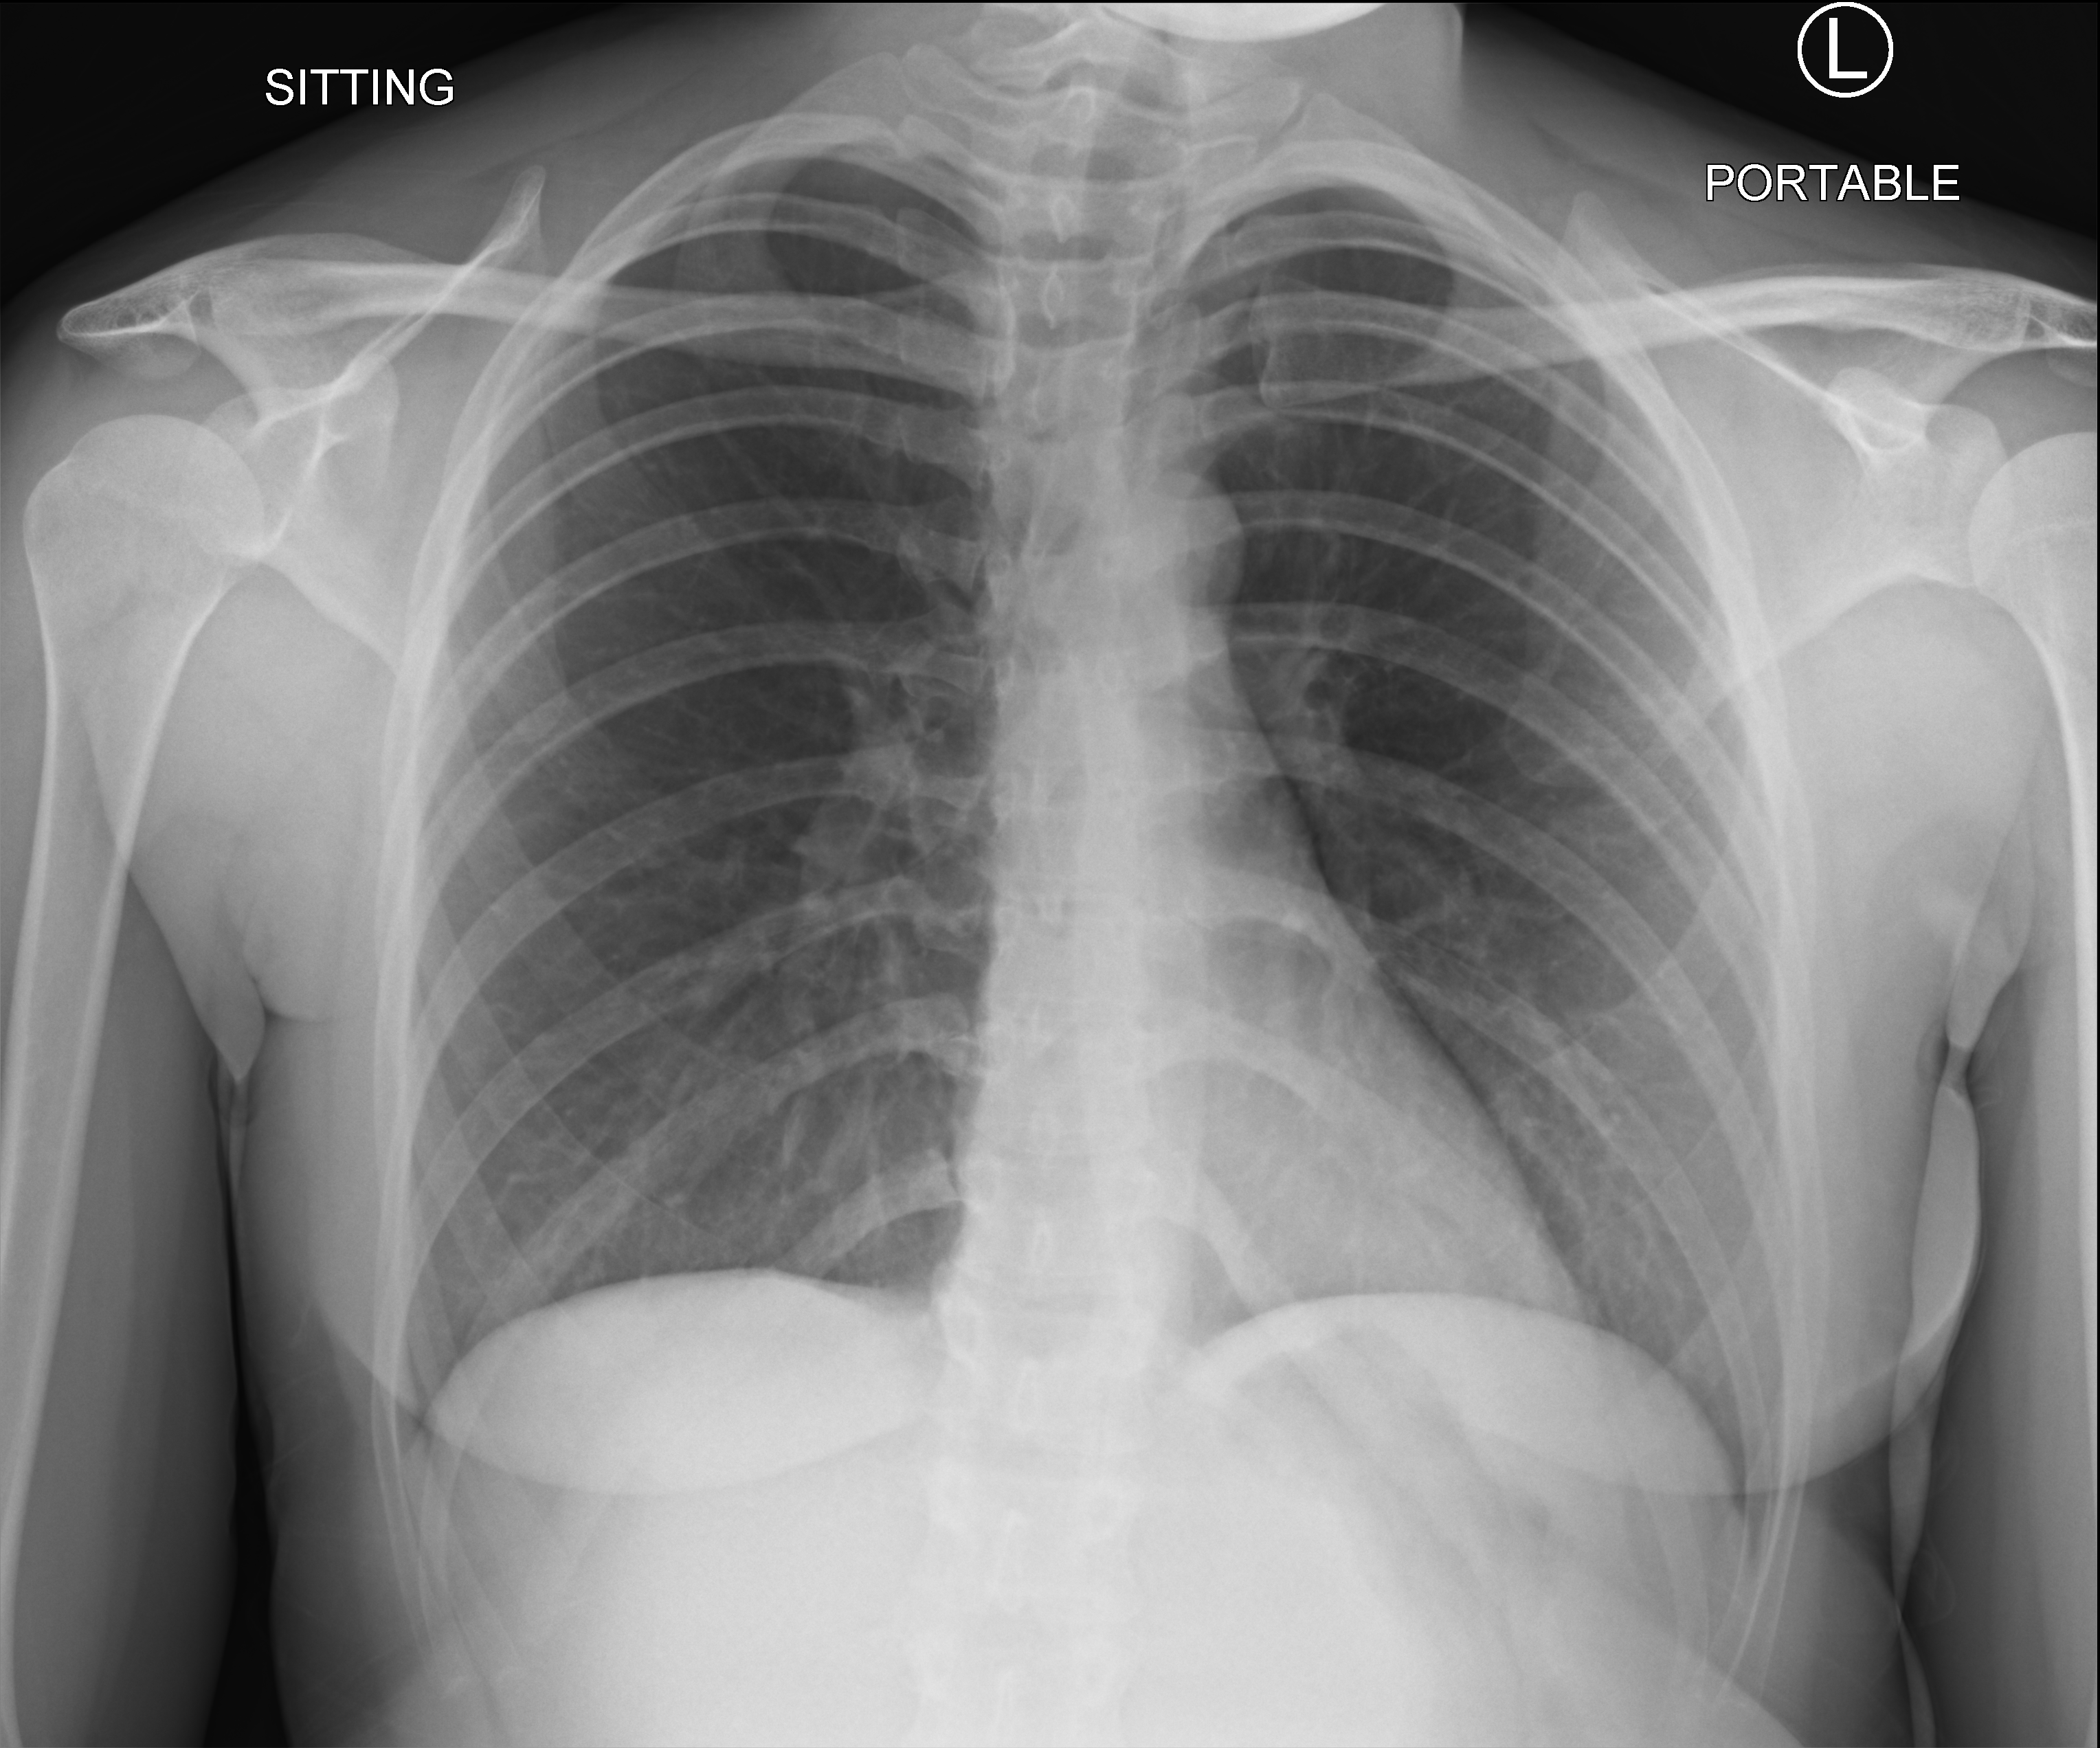
Bedside chest radiograph (computed radiography); anteroposterior (AP) projection. Female patient hospitalised with COVID-19, age 18–59 years.
Hospital-stay facts (about this admission, not read from this image; timing relative to this image not recorded): mechanically ventilated during this hospital stay: no; admitted to intensive care during this hospital stay: no.